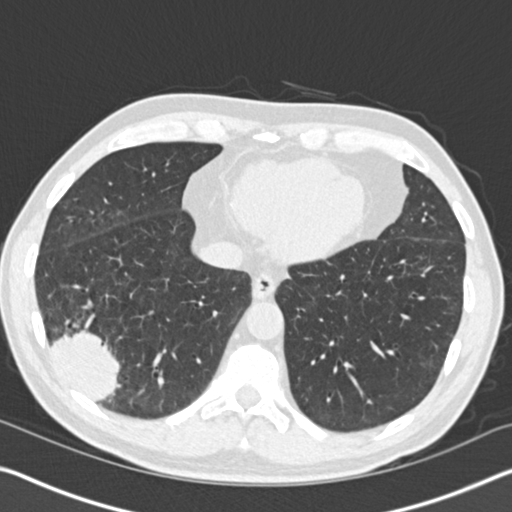
Axial slice from a low-dose chest CT screening exam. First (baseline) screen. Lung window (W 1500 / L -600 HU). 2 mm slice thickness. 120 kVp. Slice 115 of 161 in the series. Male, age 61 years at enrolment. Current smoker at enrolment.
Expert-annotated lung lesion, box from (x=22, y=291) to (x=143, y=417) px. Screening reader's record for this exam (one nodule recorded; not confirmed to be the boxed lesion): non-calcified nodule or mass ≥4 mm, right lower lobe, 52 × 36 mm, spiculated (stellate) margins, soft tissue attenuation. Official screen result: positive, change unspecified: nodule(s) >= 4 mm or enlarging nodule(s), mass(es), or other non-specific abnormalities suspicious for lung cancer. Later outcome: lung cancer diagnosed 392 days after this screen — bronchiolo-alveolar adenocarcinoma, NOS, right lower lobe, moderately differentiated (G2), stage IIIB (AJCC 6th edition), 90 mm at pathology.